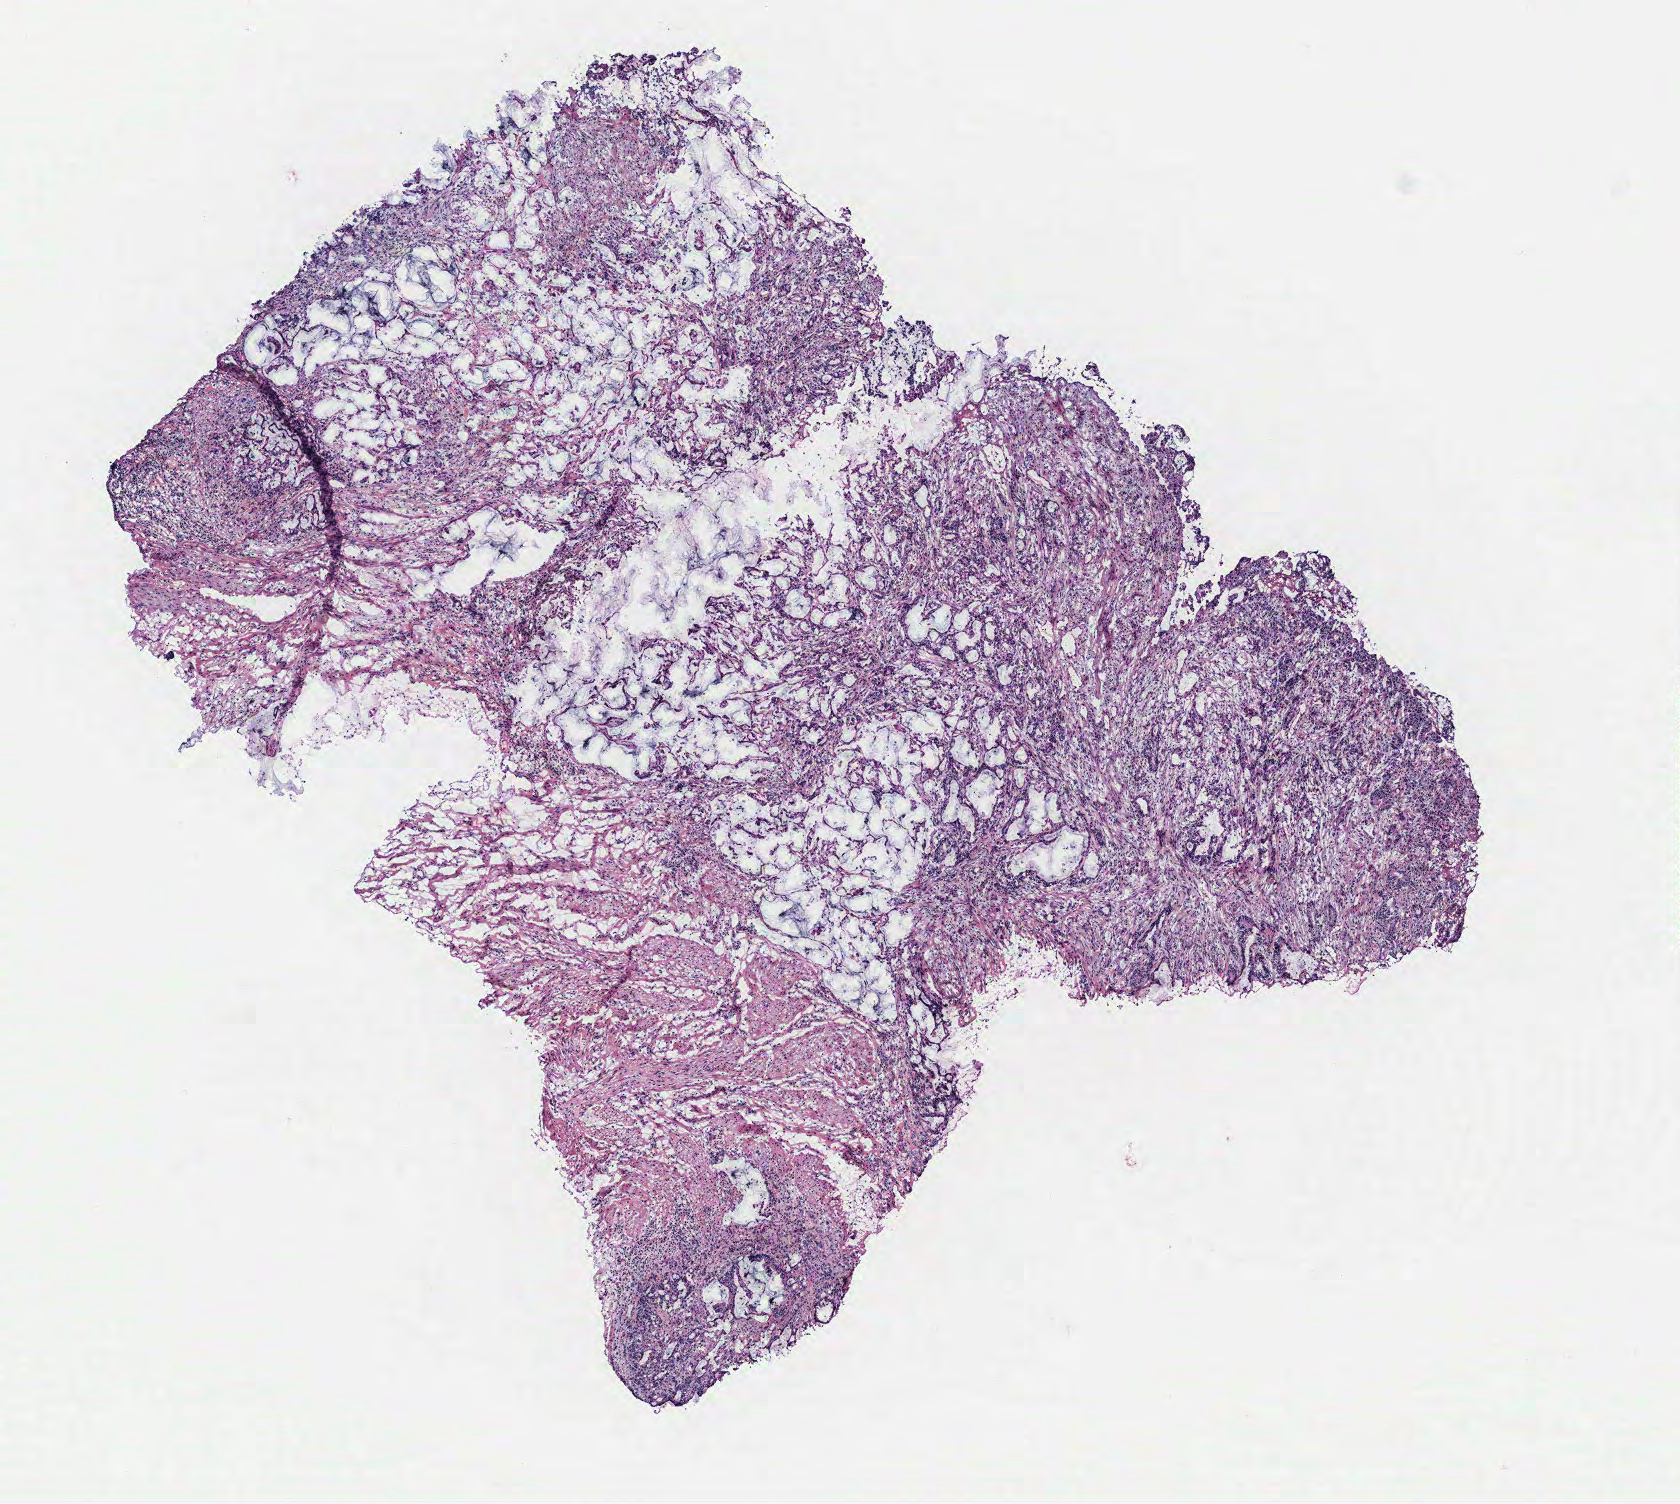
Digitized H&E tissue section (whole slide), shown as a low-resolution overview of the whole scanned area (about 6.7 x 6.0 mm, from a 40x scan). Tumour tissue sample, colon. Male, 61 y/o.
Primary tumour site (as recorded): colon. Diagnosis: Adenocarcinoma, NOS. AJCC pathologic stage: IIIC.